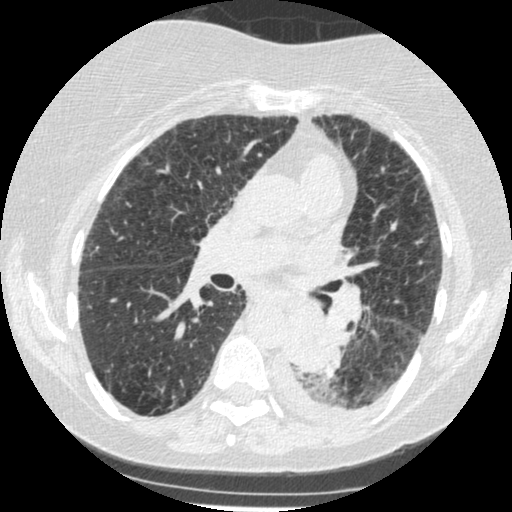
Chest CT (low-dose screening protocol), one axial image; third screening round (two years after baseline); lung window (W 1500 / L -600 HU); standard (soft-tissue) reconstruction kernel (STANDARD); slice 203 of 341 in the series. Female, age 60 years at enrolment.
Lesion marked by an expert reader, bounding box [x1, y1, x2, y2] px = [271, 306, 342, 373]. Screening reader's record for this exam (one nodule recorded; not confirmed to be the boxed lesion): non-calcified nodule or mass ≥4 mm, left lower lobe, 54 × 38 mm, smooth margins, soft tissue attenuation, pre-existing on the prior screen: yes; interval growth: yes. Participant outcome: lung cancer diagnosed 15 days after this screen — small cell carcinoma, NOS, left lower lobe, undifferentiated (G4), stage IV (AJCC 6th edition), 69 mm at pathology.